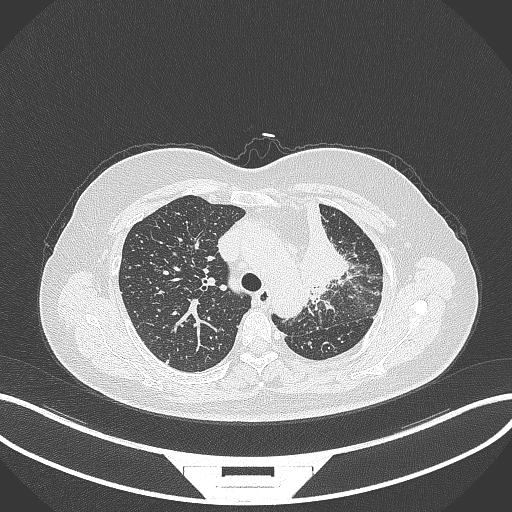
Chest CT, one axial slice. Position 243 of 348 along the scan axis. 120 kVp. Lung window (W 1500 / L -600 HU). 1 mm slice thickness. 512 × 512 image matrix. Patient: female, 49 years. From the clinical record (not read from this slice): clinical TNM (as recorded): T1c N0 M1.
Structures marked on this image (bounding box drawn by a radiologist):
- lung tumour (recorded histology: adenocarcinoma): box from (x=299, y=211) to (x=350, y=302) px